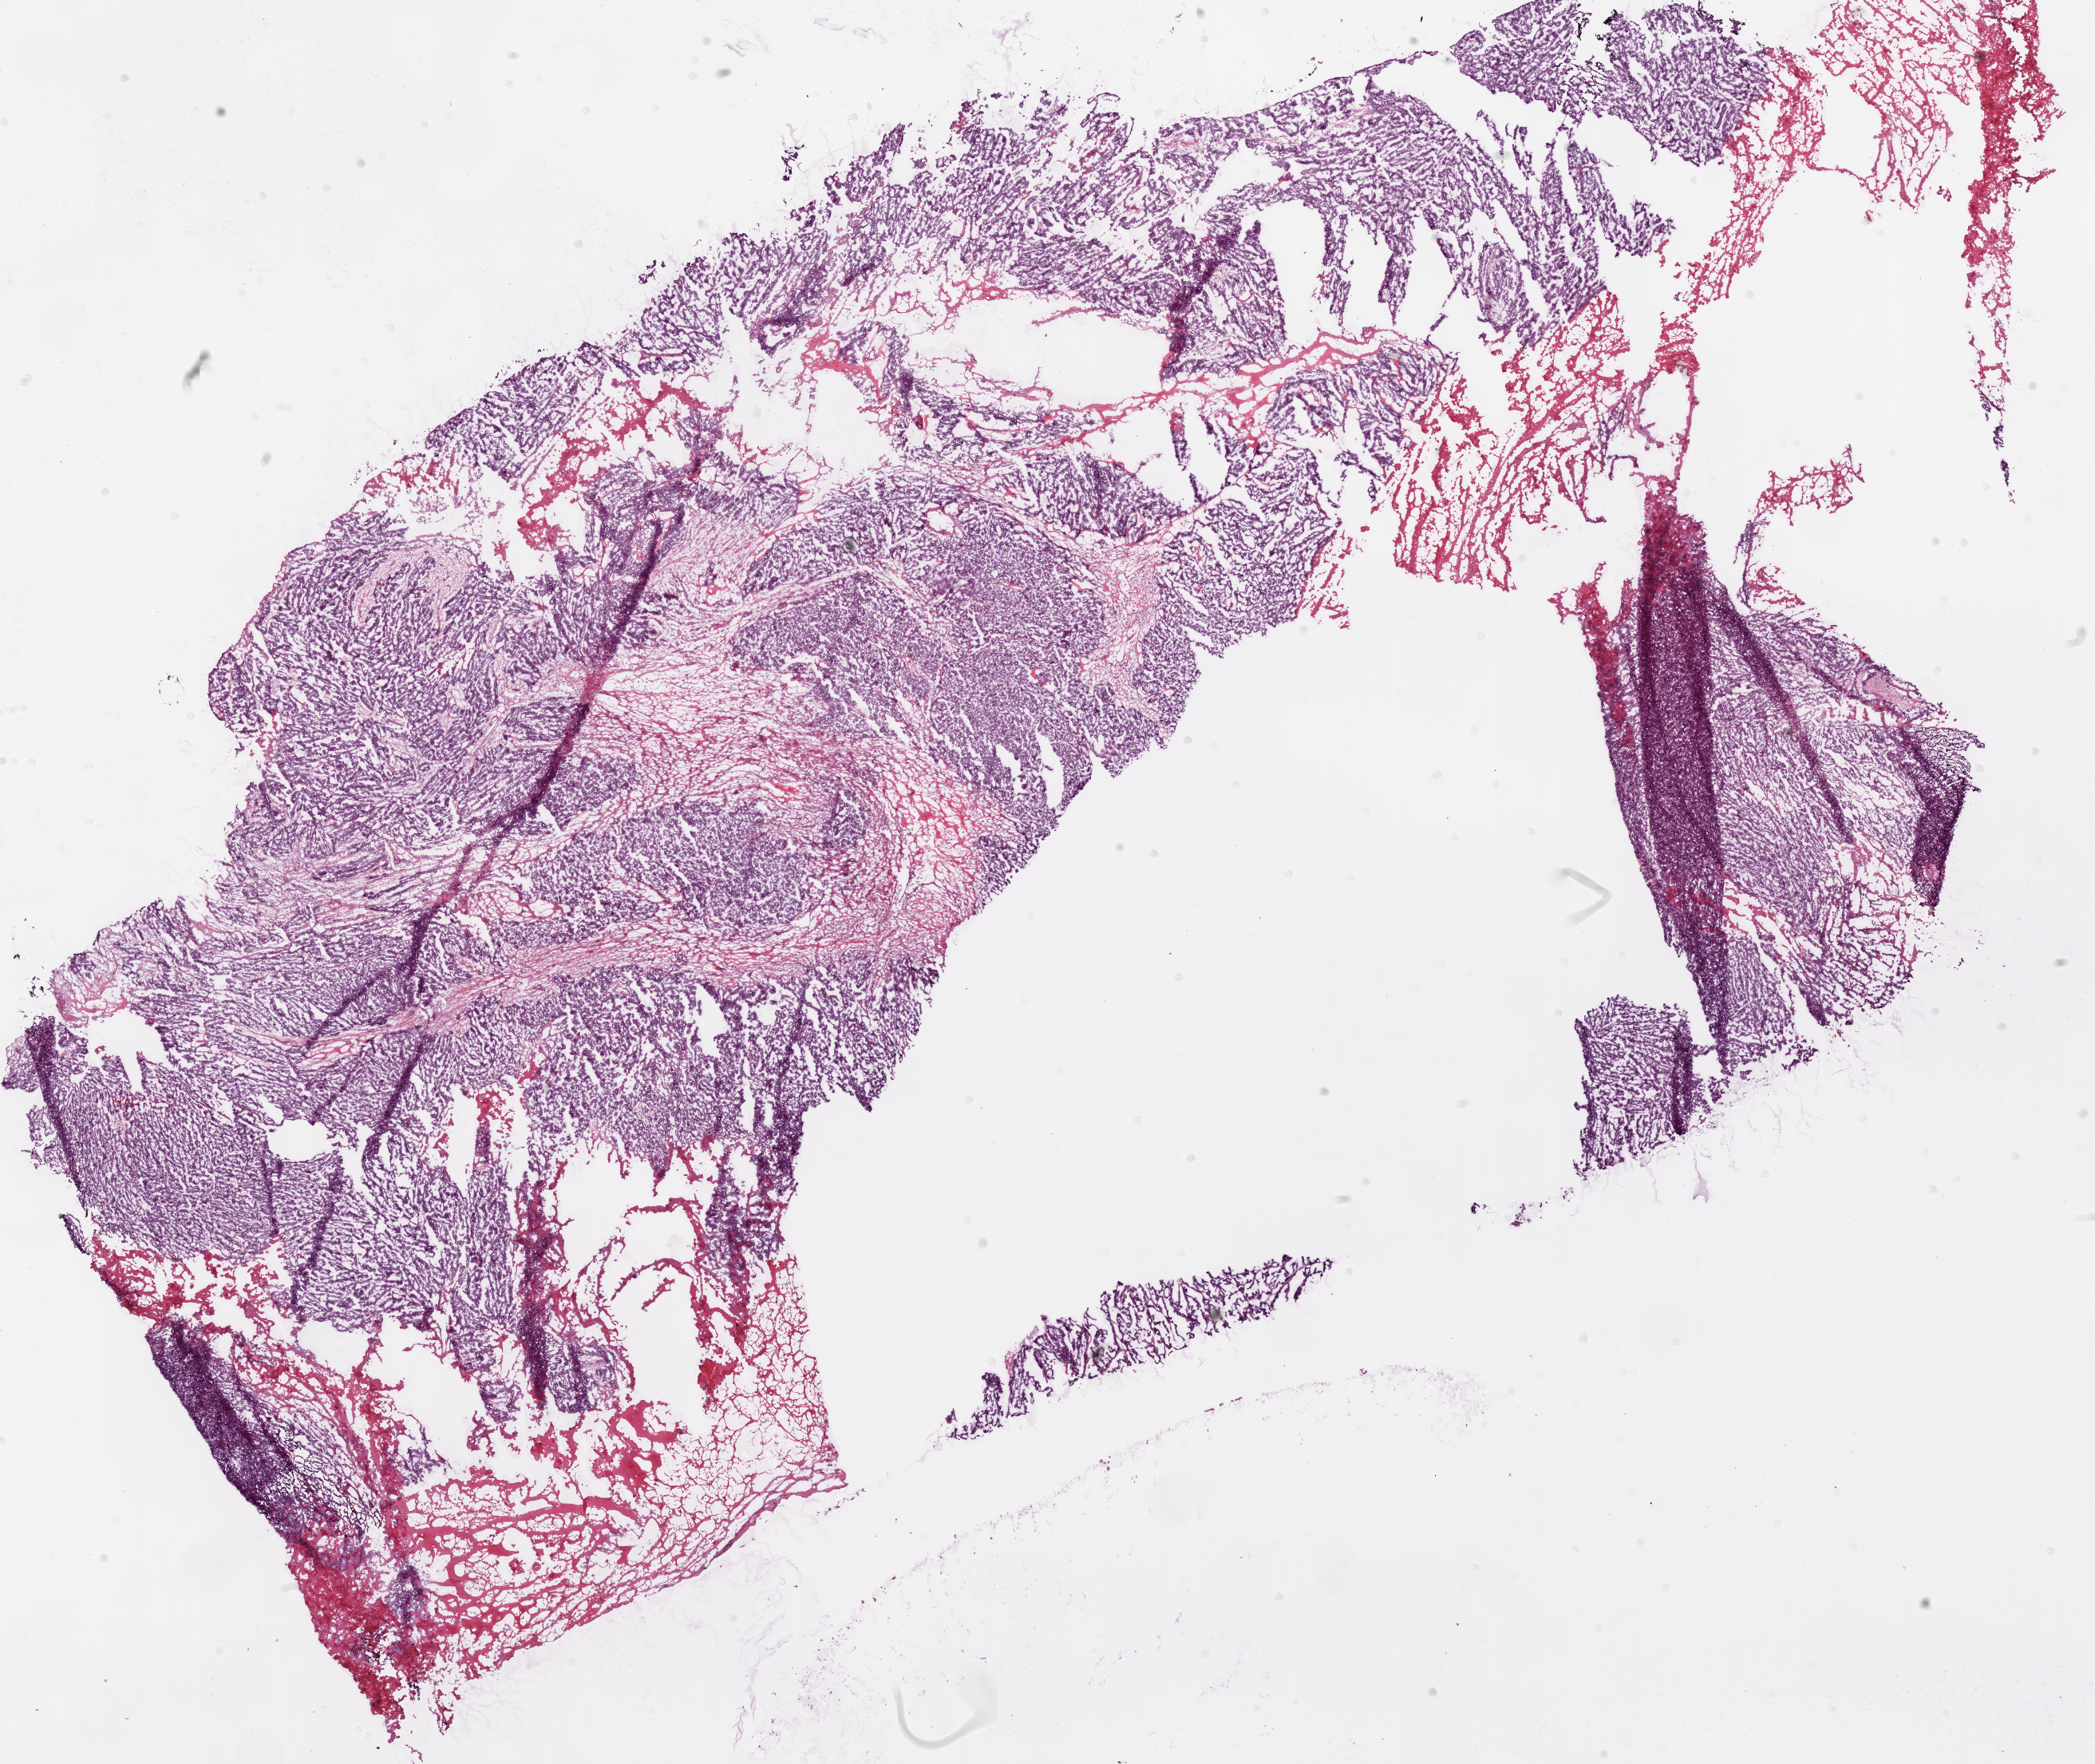
Whole-slide histology image, H&E-stained, a low-resolution overview of the entire scanned area, about 21.1 x 17.7 mm, frozen section from the bottom of the tissue portion, sample: primary tumour, ovary. Female, age 62 years at initial diagnosis. Histologic grade: G3 (poorly differentiated). Composition of this section per pathologist review: tumour cells 75%, tumour nuclei 95%, normal cells 0%, stromal cells 5%, necrosis 20%.
Histologic diagnosis: Serous cystadenocarcinoma, NOS. FIGO stage: IIIC. Laterality: left.